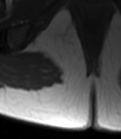
MRI of an extremity soft-tissue mass, one axial slice; slice 34 of 47 in the series (ordered by position); MR volume resampled by the dataset authors to the PET/CT grid (not the native acquisition matrix); 3.27 mm slice thickness; 121 × 139 image matrix, field of view 118 × 136 mm. Female patient. Case-level facts recorded for this patient, not image findings: histological type: epithelioid sarcoma; grade: intermediate; site of the primary tumour: right buttock.
Outlined on this slice (expert contour drawn on MRI and transferred to this co-registered scan by the dataset authors):
- gross tumour volume including surrounding oedema: bounding box (x1, y1, x2, y2) in pixels: (50, 29, 69, 49)